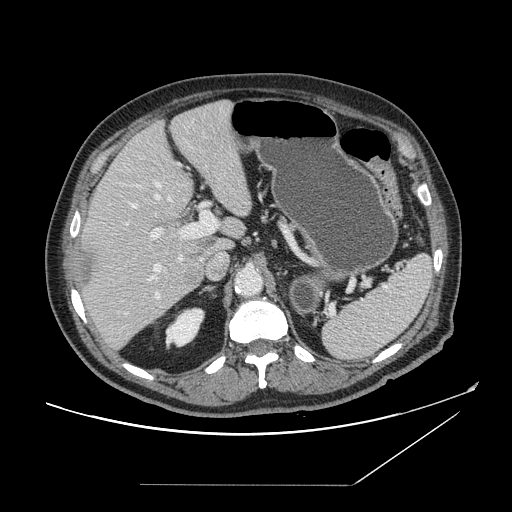
Contrast-enhanced abdominal CT, one axial slice. Intravenous contrast given. Soft-tissue window (W 400 / L 40 HU). 2.5 mm slice thickness. 512 × 512 image matrix, field of view 416 × 416 mm. Male patient, age 80 years. Case-level facts recorded for this patient, not image findings: diagnosis: colorectal cancer liver metastases, imaged before liver resection; multiple liver metastases: no; largest metastasis: 2.2 cm.
Outlined on this slice (outlined manually by an expert reader):
- hepatic veins: bounding box (x1, y1, x2, y2) in pixels: (126, 182, 172, 315)
- liver: (79, 102, 253, 350)
- planned liver remnant (the part of the liver to remain after resection): (89, 101, 252, 256)
- portal vein (with intrahepatic branches): (131, 204, 219, 298)
- liver metastasis: (83, 250, 96, 286)